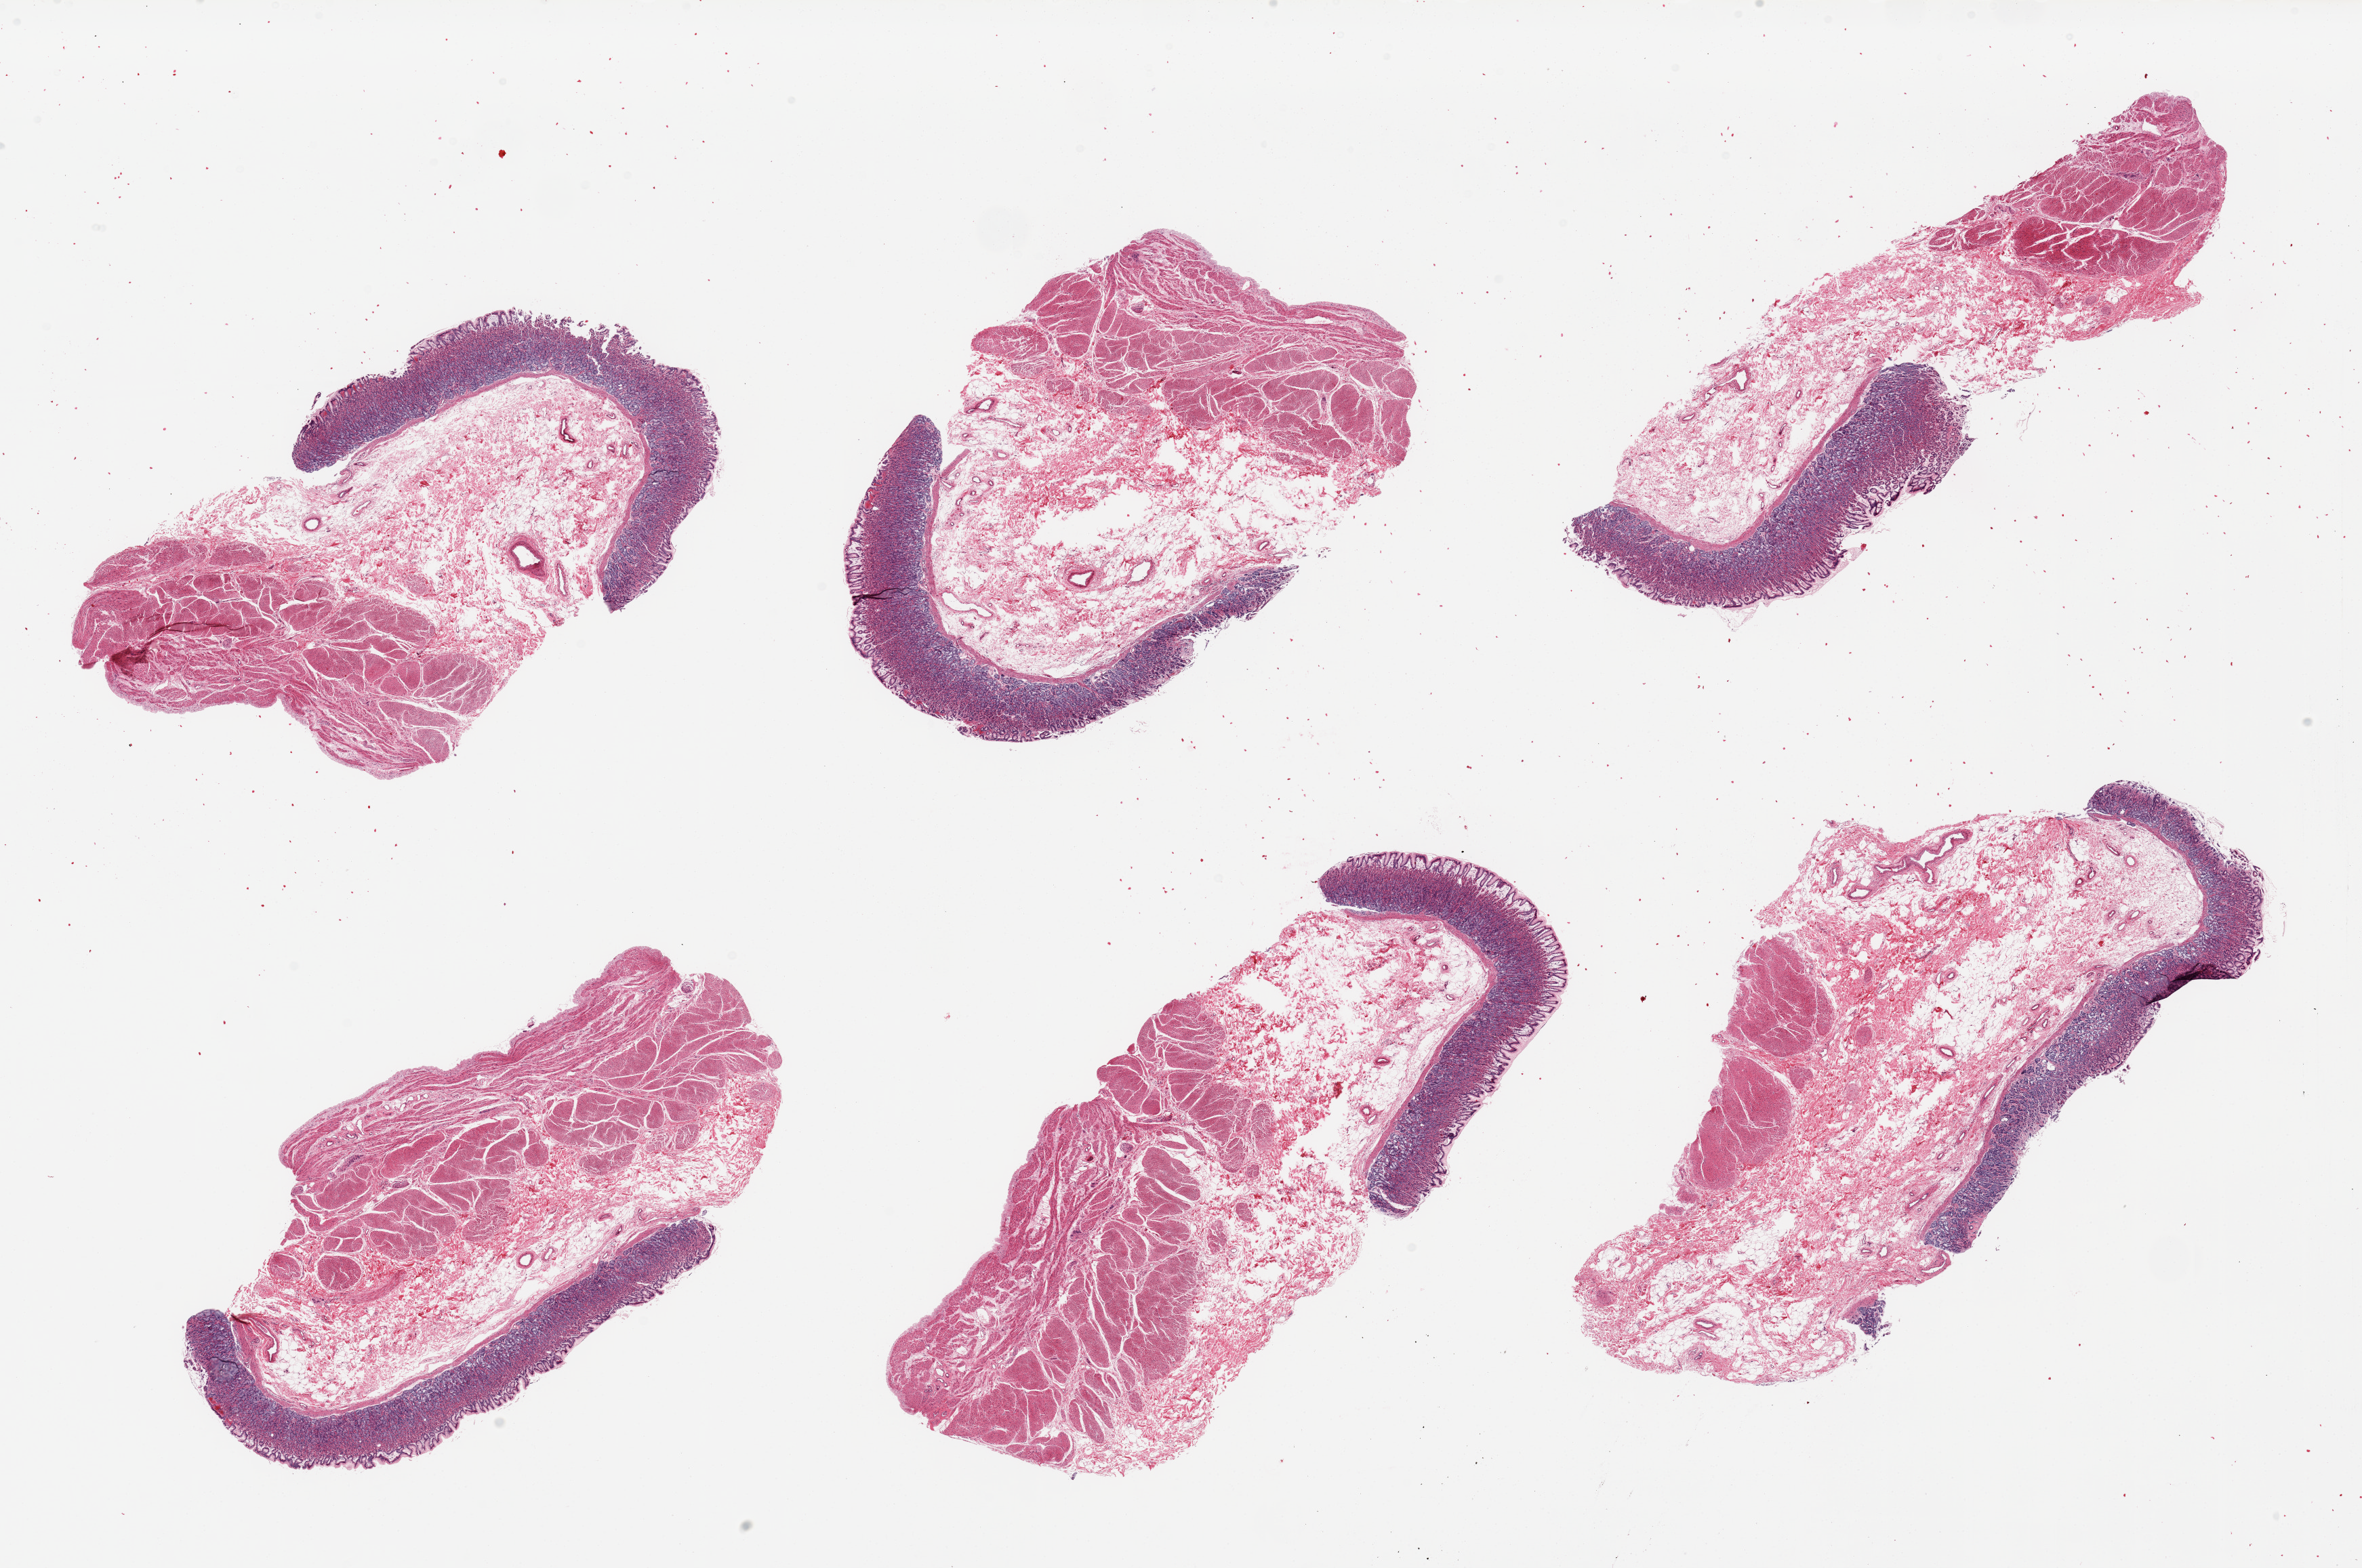
Digitized hematoxylin and eosin (H&E)-stained section, a low-resolution overview of the entire scanned area, about 27.6 x 18.3 mm. PAXgene-fixed paraffin-embedded (PFPE) section. Section of stomach (target tissue). Tissue donor sample. Male donor.
• pathologist's review note for this sample: 6 pieces; well preserved mucosa and muscle with some surface loss